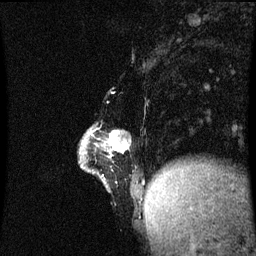
Breast MRI (dynamic contrast-enhanced), one sagittal slice. Position 17 of 60 along the scan axis. Dynamic contrast-enhanced series, image 2 of 3 at this slice position (ordered by acquisition). 1.5 T. TE 4.2 ms, TR 8.9 ms. 2 mm slice thickness. 256 × 256 image matrix, field of view 200 × 200 mm. Female patient, age 47 years. From the clinical record (not read from this slice): setting: breast cancer imaged before/during neoadjuvant chemotherapy; receptor status: HR-positive, HER2-negative.
Outlined on this slice (semi-automatically segmented with operator editing):
- analysis volume of interest (the breast-tissue region the enhancement analysis was run in; not a lesion): bounding box [x1, y1, x2, y2] px = [82, 128, 148, 199]
- tumour enhancement mask (voxels above the 70 % enhancement threshold inside the analysis volume of interest): [112, 134, 129, 149]